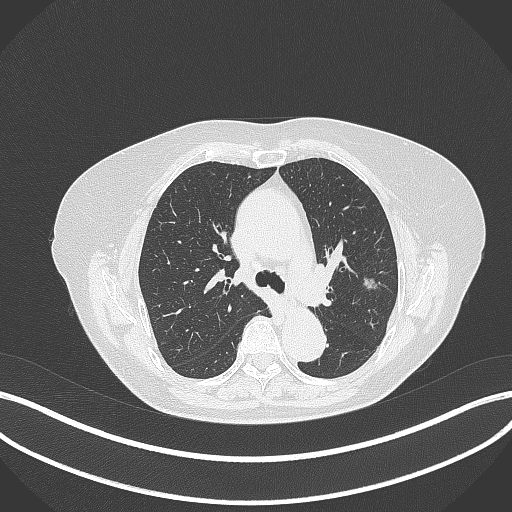
Chest CT, one axial slice; slice 218 of 316 in the series (ordered by position); reconstruction kernel B70f; 120 kVp; lung window (W 1500 / L -600 HU); 1 mm slice thickness; 512 × 512 image matrix, field of view 400 × 400 mm. Patient: female, 75 years. Case-level facts recorded for this patient, not image findings: clinical TNM (as recorded): T1c N0 M0.
Structures marked on this image (bounding box drawn by a radiologist):
- lung tumour (recorded histology: adenocarcinoma): box from (x=361, y=275) to (x=380, y=293) px